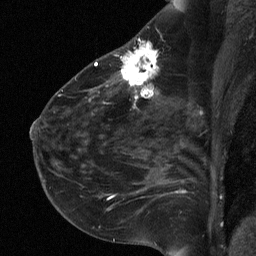
Breast MRI (dynamic contrast-enhanced), one sagittal slice; position 39 of 64 along the scan axis; dynamic contrast-enhanced study with each time point stored as its own series, time point 2 of 3 at this slice position (early post-contrast, ordered by acquisition time); 1.5 T; TE 4.8 ms, TR 27 ms; 2 mm slice thickness; 256 × 256 image matrix, field of view 180 × 180 mm. Female patient, age 51 years. From the clinical record (not read from this slice): setting: breast cancer imaged before/during neoadjuvant chemotherapy; receptor status: HR-positive, HER2-negative.
Annotated regions visible in this slice (semi-automatic segmentation, software-assisted and operator-edited):
- analysis volume of interest (the breast-tissue region the enhancement analysis was run in; not a lesion): bounding box (x1, y1, x2, y2) in pixels: (72, 34, 182, 118)
- tumour enhancement mask (voxels above the 90 % enhancement threshold inside the analysis volume of interest): (95, 42, 159, 107)